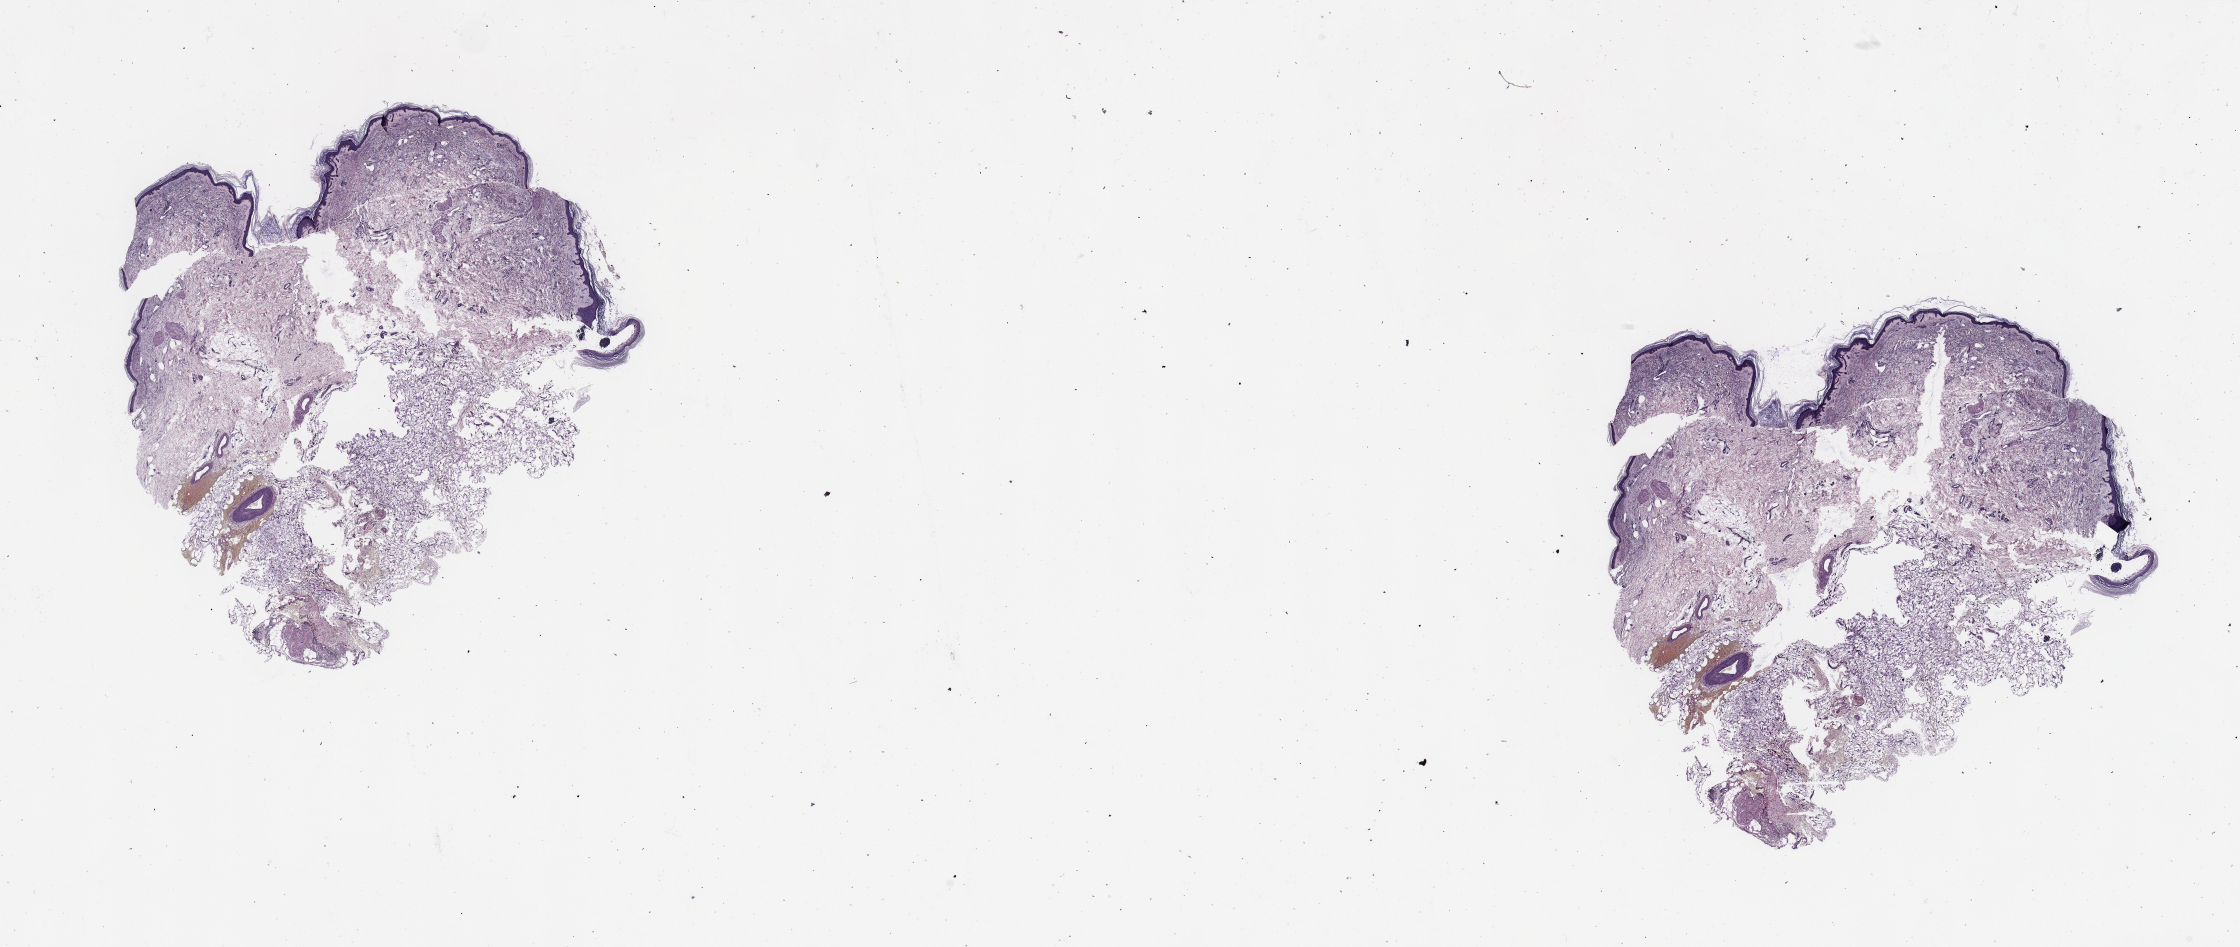
Digitized H&E-stained tissue section (whole slide) — a low-resolution overview of the entire scanned area, about 35.4 x 15.0 mm (acquisition: 20x scan); melanoma tumour tissue; sampled site not recorded. Patient: female, age 78 years.
- AJCC pathologic stage: IIB
- primary tumour site (as recorded): extremities
- histologic diagnosis: Malignant melanoma, NOS